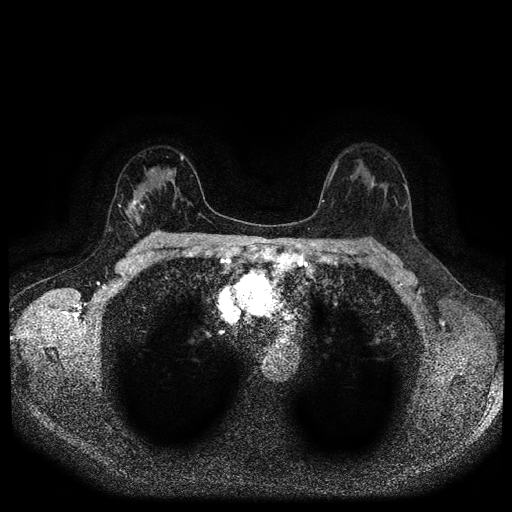
Breast MRI (dynamic contrast-enhanced, multi-phase), one axial slice. Slice 65 of 116 in the series (ordered by position). Dynamic contrast-enhanced series, time point 2 of 5 at this slice position (early post-contrast). 1.5 T. TE 2.7 ms, TR 5.4 ms. 512 × 512 image matrix. Patient: female, 42 years.
Annotated regions visible in this slice (semi-automatically segmented with operator editing):
- breast lesion (labelled 'tumour' in the annotation; benign lesions carry a separate 'benign' label): bounding box [x1, y1, x2, y2] px = [126, 196, 146, 223]